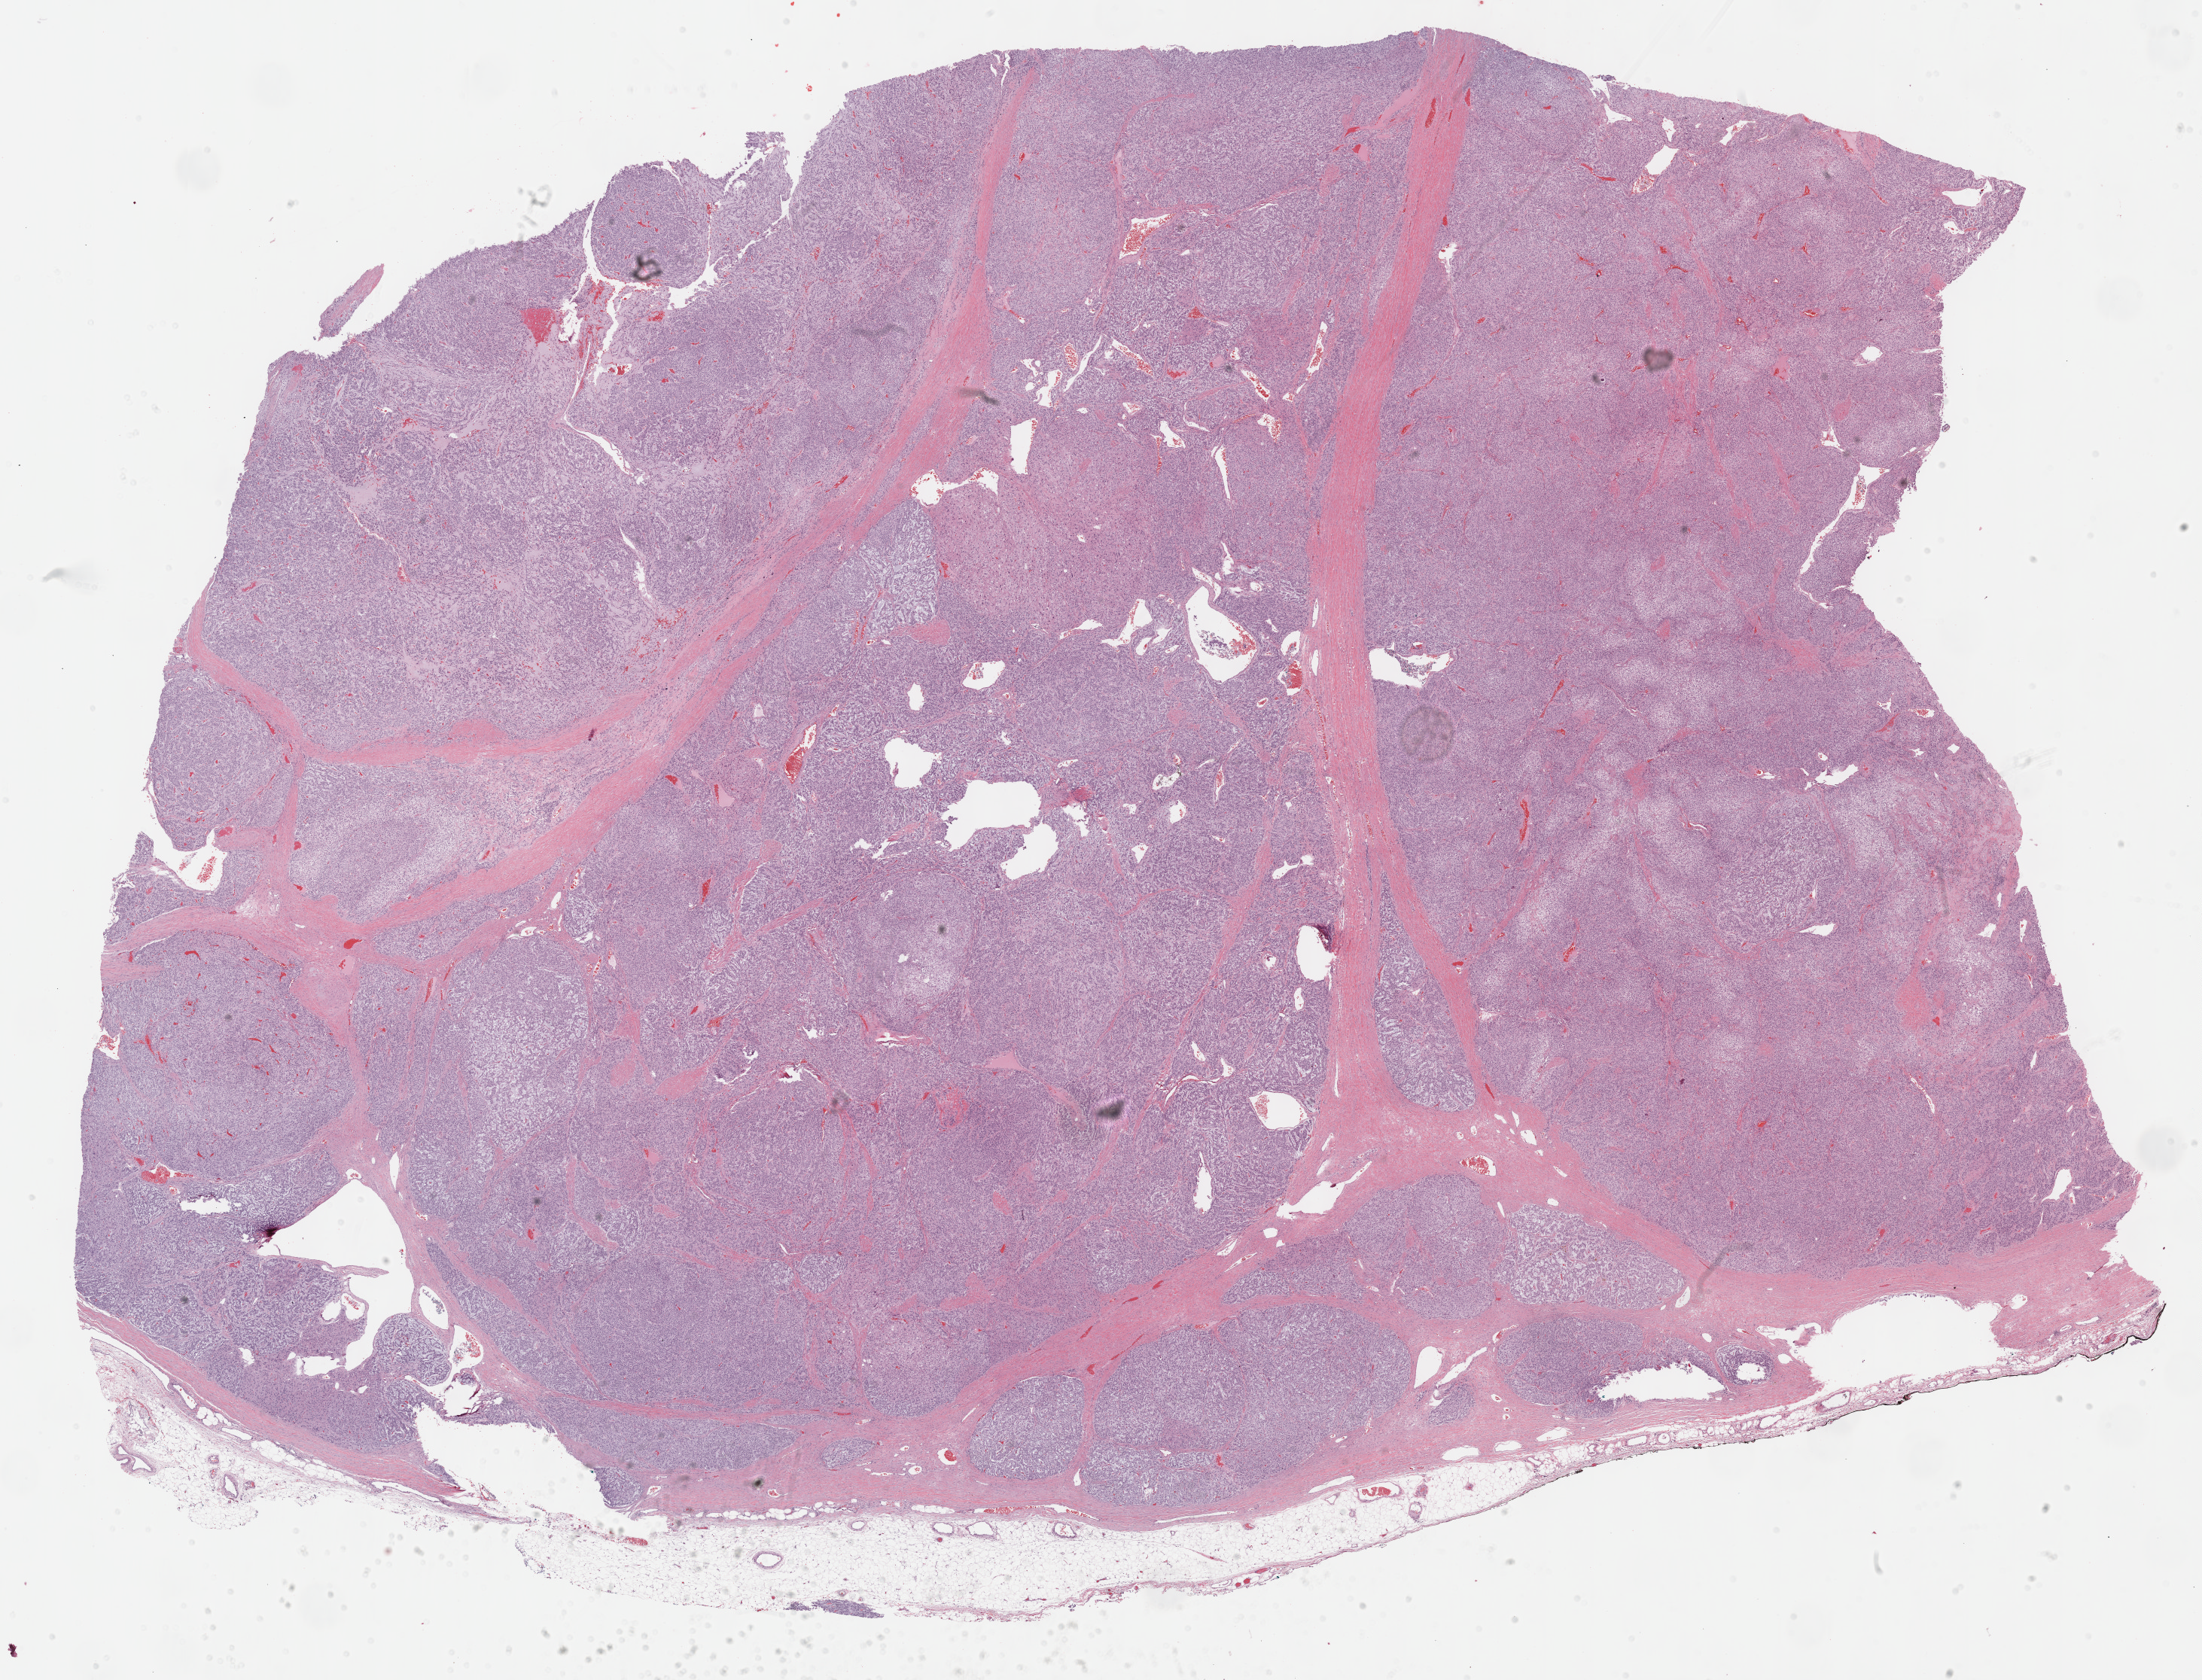
Hematoxylin and eosin (H&E) stained whole-slide image, shown as a low-resolution overview of the whole scanned area (about 23.7 x 18.1 mm, acquisition: 40x scan). Formalin-fixed paraffin-embedded (FFPE) diagnostic section. Adrenal cortex, primary tumour sample. Patient: male, age at initial diagnosis 50 years.
Laterality: left. Histologic diagnosis: Adrenal cortical carcinoma (cortex of adrenal gland). Lymph nodes positive (case pathology): 0 of 1 examined.